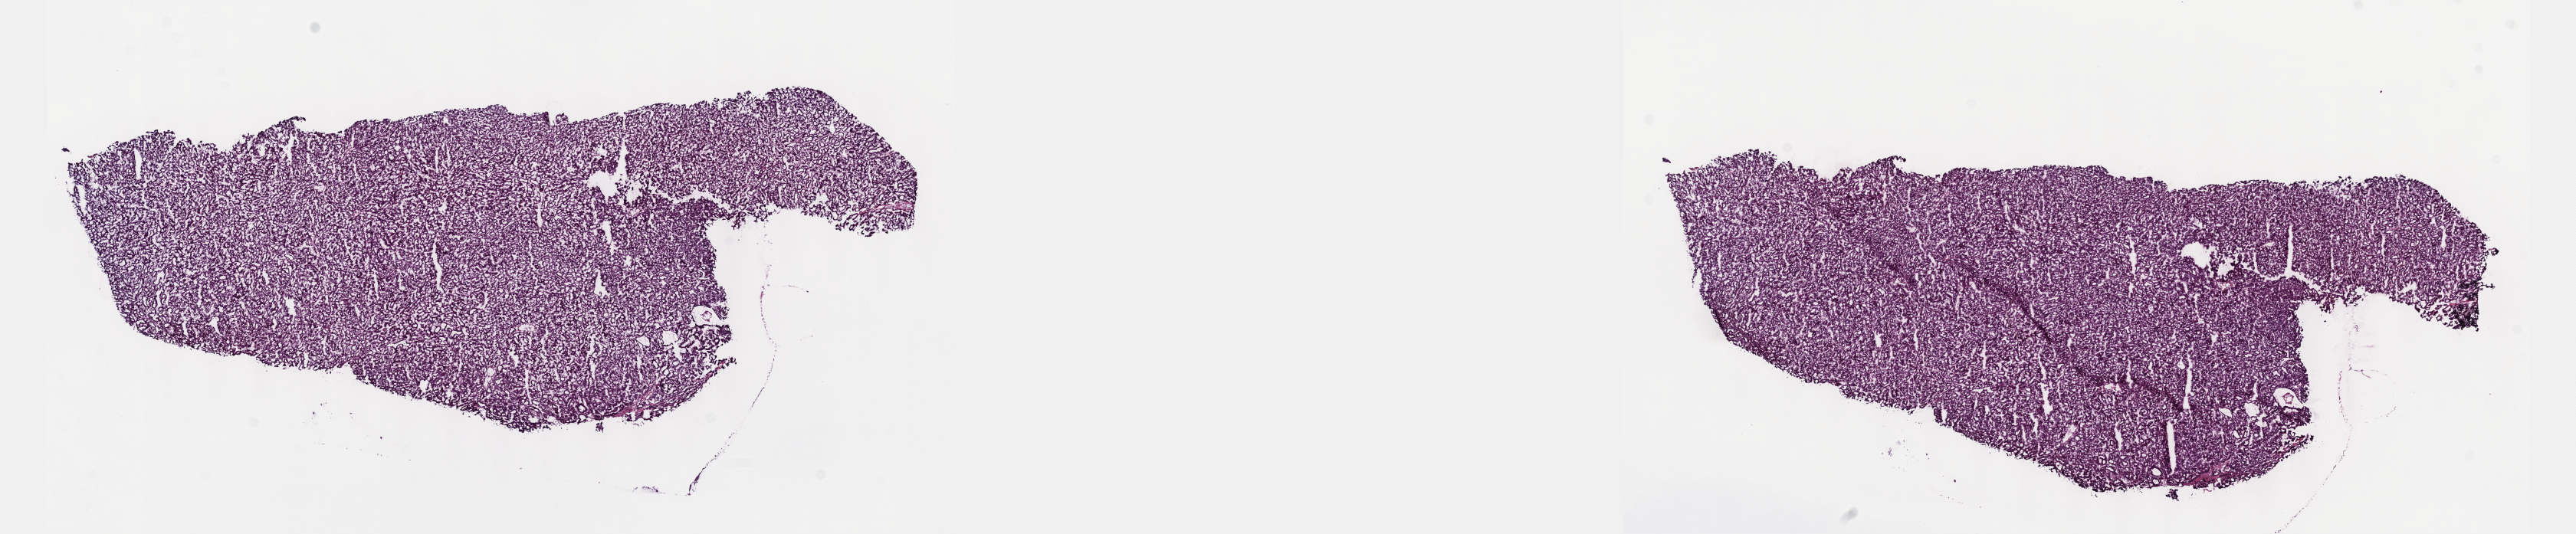
H&E whole-slide image, whole scanned area (about 27.2 x 5.6 mm, acquisition: 40x scan) shown as a low-resolution overview; frozen section; liver, primary tumour sample. Male, age 50 years at initial diagnosis. Histologic grade: G4 (undifferentiated). Composition of this section per pathologist review: tumour cells 80%, tumour nuclei 80%, normal cells 0%, stromal cells 20%, necrosis 0%. Inflammatory infiltration, as recorded: lymphocyte infiltration 3%, monocyte infiltration 1%, neutrophil infiltration 1%.
Histologic diagnosis: Hepatocellular carcinoma, NOS. AJCC pathologic stage: I (7th edition).